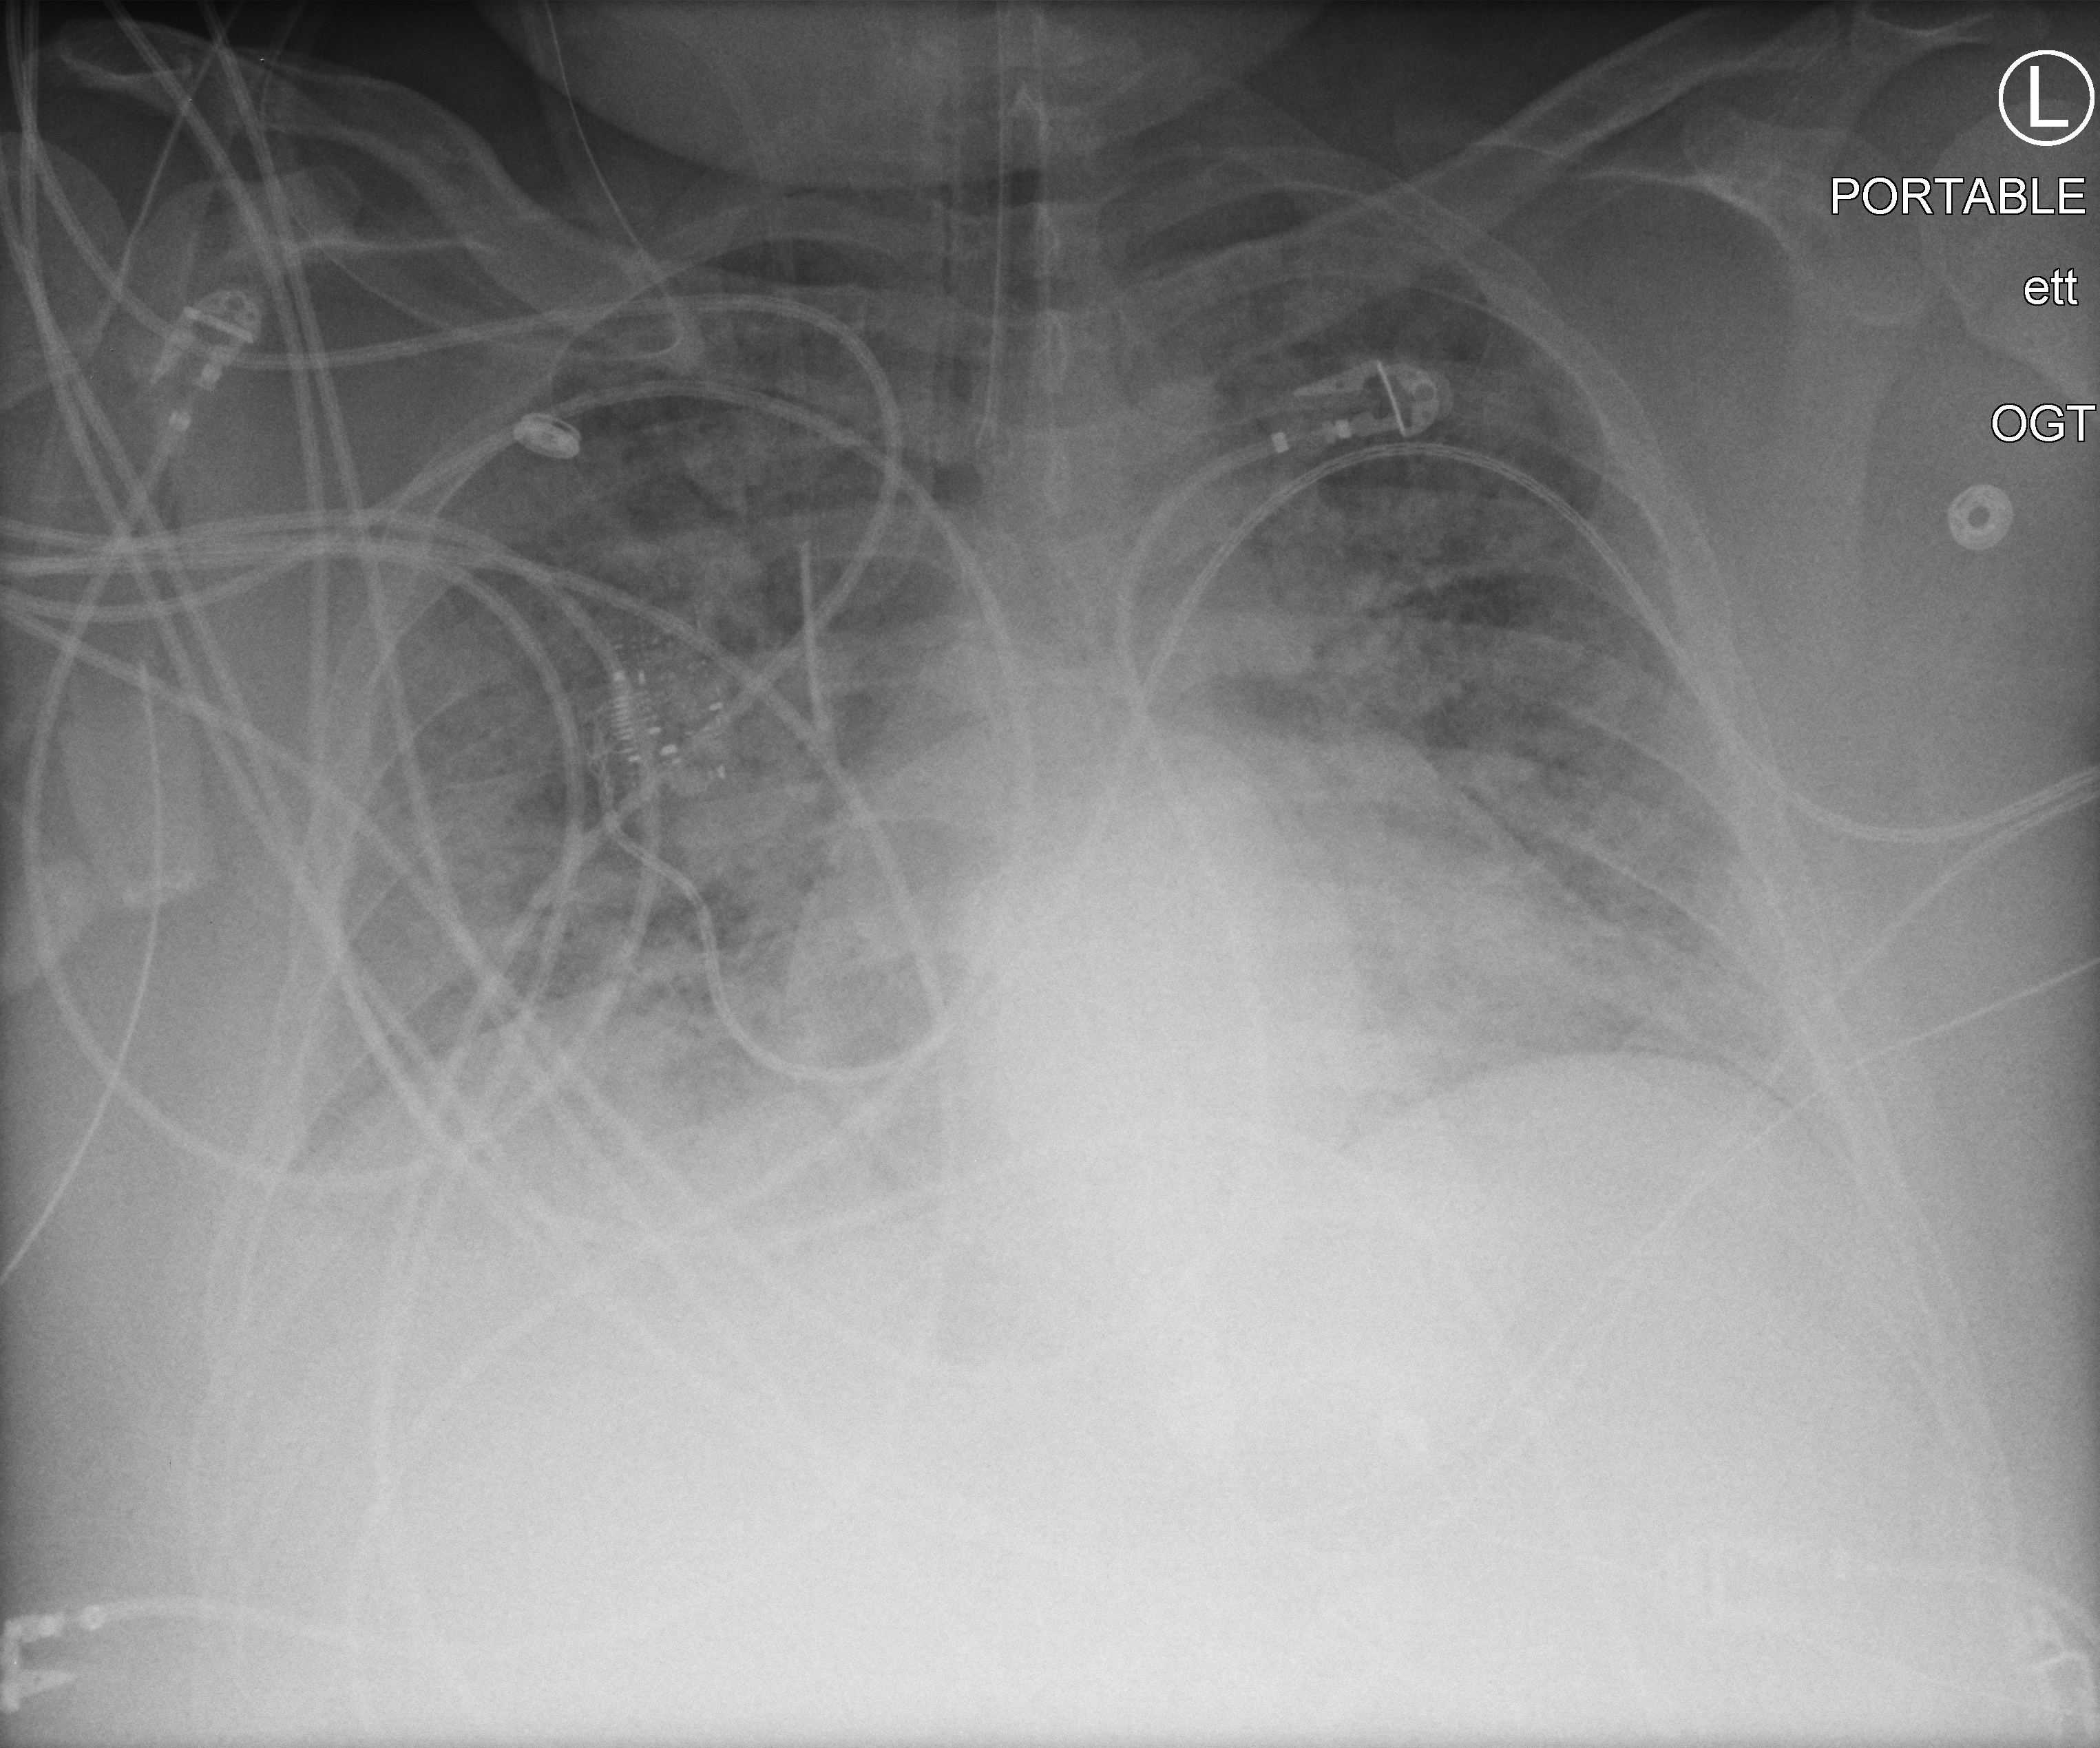
Portable chest radiograph. Patient hospitalised with COVID-19, aged 18–59 years.
Hospital-stay facts (about this admission, not read from this image; timing relative to this image not recorded):
- length of hospital stay: 22 days
- mechanically ventilated during this hospital stay: yes